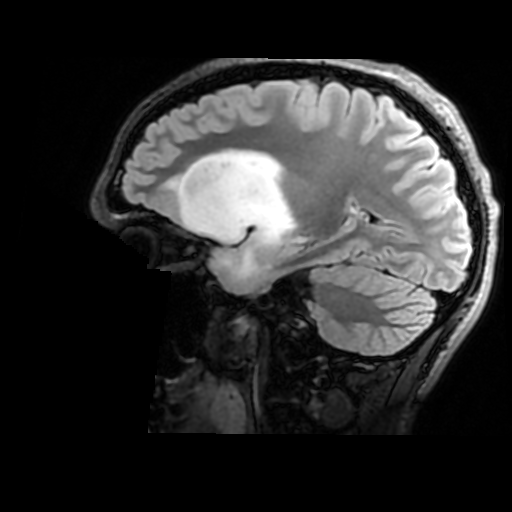
Brain MRI from a brain-tumour surgery series, one sagittal slice; slice 111 of 176 in the series (ordered by position); T2 FLAIR; 1 mm slice thickness; 512 × 512 image matrix, field of view 240 × 240 mm. From the clinical record (not read from this slice): histopathology: Astrocytoma; WHO grade: 2.
Annotated regions visible in this slice (manually delineated by an expert):
- tumour: bounding box <176,149,293,285> (left, top, right, bottom; pixels)